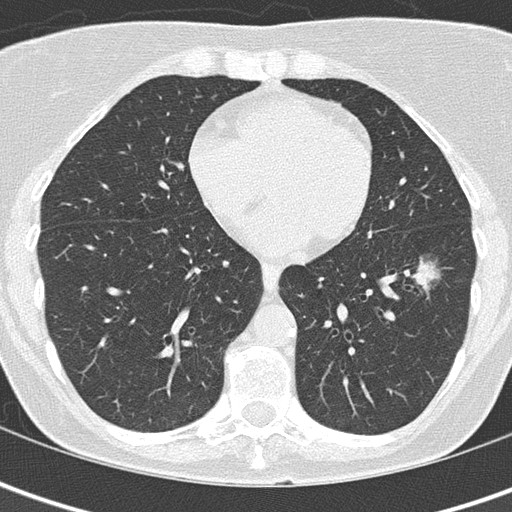
Low-dose screening chest CT, one axial slice. Slice 58 of 149 in the series (ordered by position). Reconstruction kernel B50f. Lung window (W 1500 / L -600 HU). 2 mm slice thickness. 512 × 512 image matrix, field of view 280 × 280 mm.
Outlined on this slice (expert manual segmentation):
- lesion 1 (tumor, lower lobe of left lung): box from (x=414, y=261) to (x=439, y=288) px